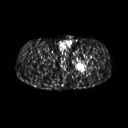
FDG PET of an extremity soft-tissue mass (from a PET/CT study), one axial slice; 128 × 128 image matrix, field of view 500 × 500 mm. Male patient, age 27 years. Case-level facts recorded for this patient, not image findings: histological type: extraskeletal osteosarcoma; grade: high; site of the primary tumour: left adductur.
Structures marked on this image (expert contour drawn on MRI and transferred to this co-registered scan by the dataset authors):
- gross tumour volume (mass): bounding box (x1, y1, x2, y2) in pixels: (72, 52, 95, 75)